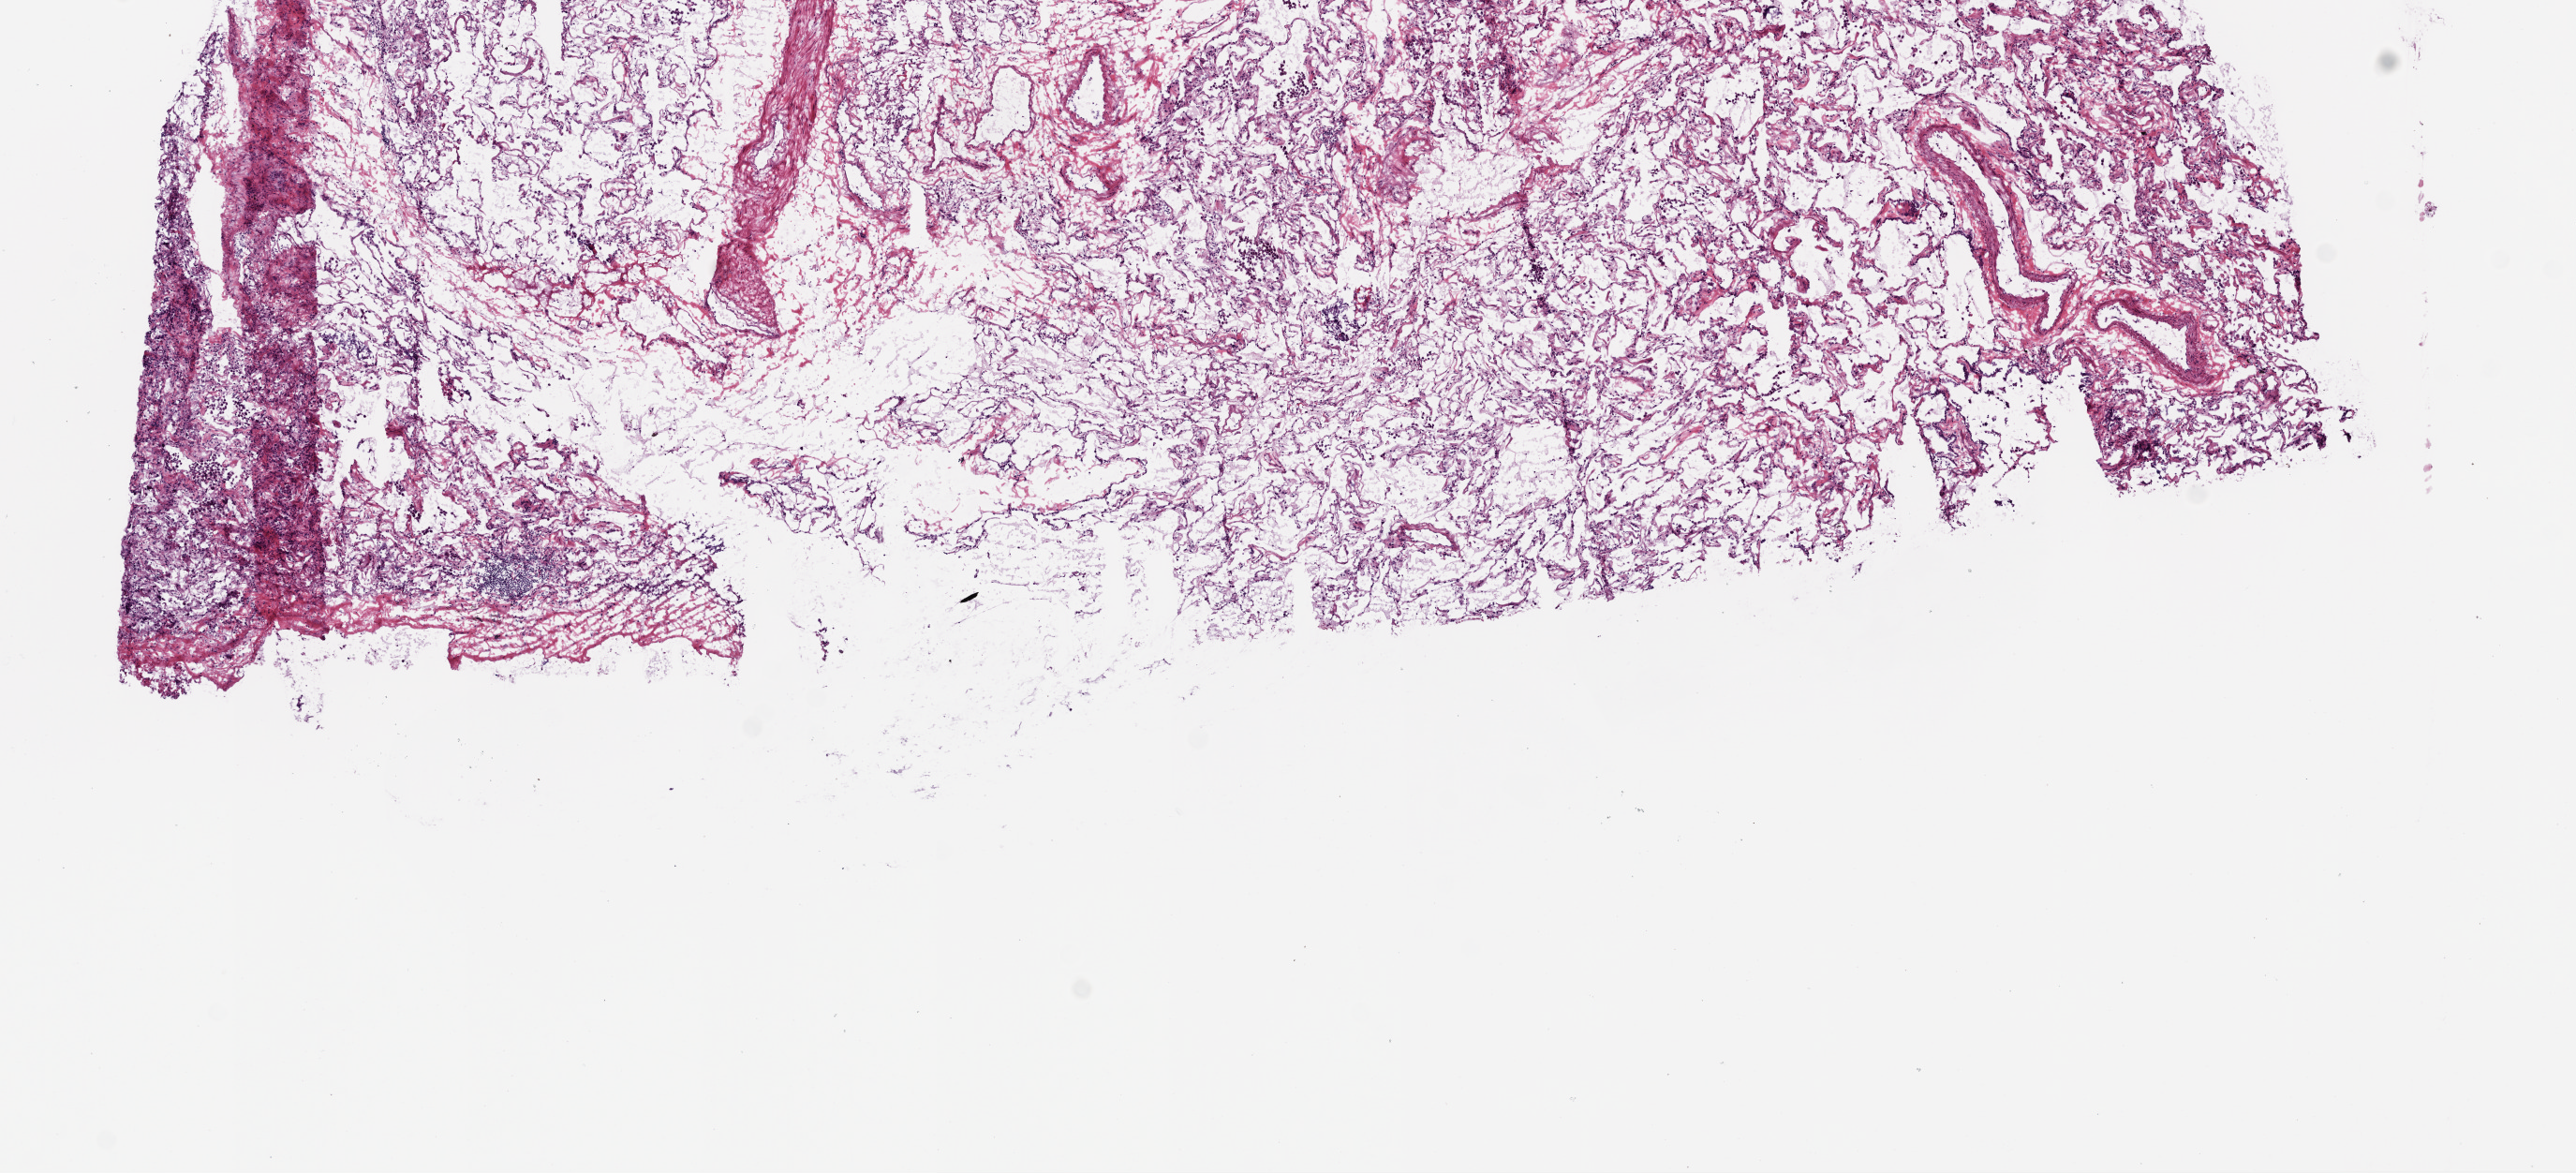
Whole-slide histology image, Hematoxylin and eosin (H&E) stained, shown as a low-resolution overview of the whole scanned area (about 11.0 x 5.0 mm, slide scanned at 20x). Frozen section from the top of the tissue portion. Lung, solid tissue normal (non-tumour tissue) sample. Patient: female, age at initial diagnosis 75 years.
This section: solid tissue normal (non-tumour) sample from the same patient. Patient diagnosis: Papillary adenocarcinoma, NOS (upper lobe, lung).